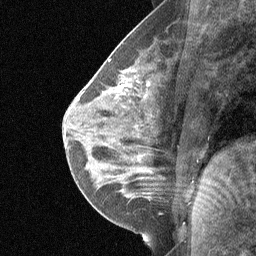
Breast MRI (dynamic contrast-enhanced), one sagittal slice; slice 31 of 64 in the series (ordered by position); dynamic contrast-enhanced study with each time point stored as its own series, time point 3 of 5 at this slice position (ordered by acquisition time); 1.5 T; TE 4.8 ms, TR 27 ms; 256 × 256 image matrix. Female patient, age 26 years. From the clinical record (not read from this slice): setting: breast cancer imaged before/during neoadjuvant chemotherapy; receptor status: HR-positive, HER2-negative.
Structures marked on this image (semi-automatic segmentation, software-assisted and operator-edited):
- analysis volume of interest (the breast-tissue region the enhancement analysis was run in; not a lesion): bounding box <85,46,171,144> (left, top, right, bottom; pixels)
- tumour enhancement mask (voxels above the 90 % enhancement threshold inside the analysis volume of interest): <116,86,121,92>